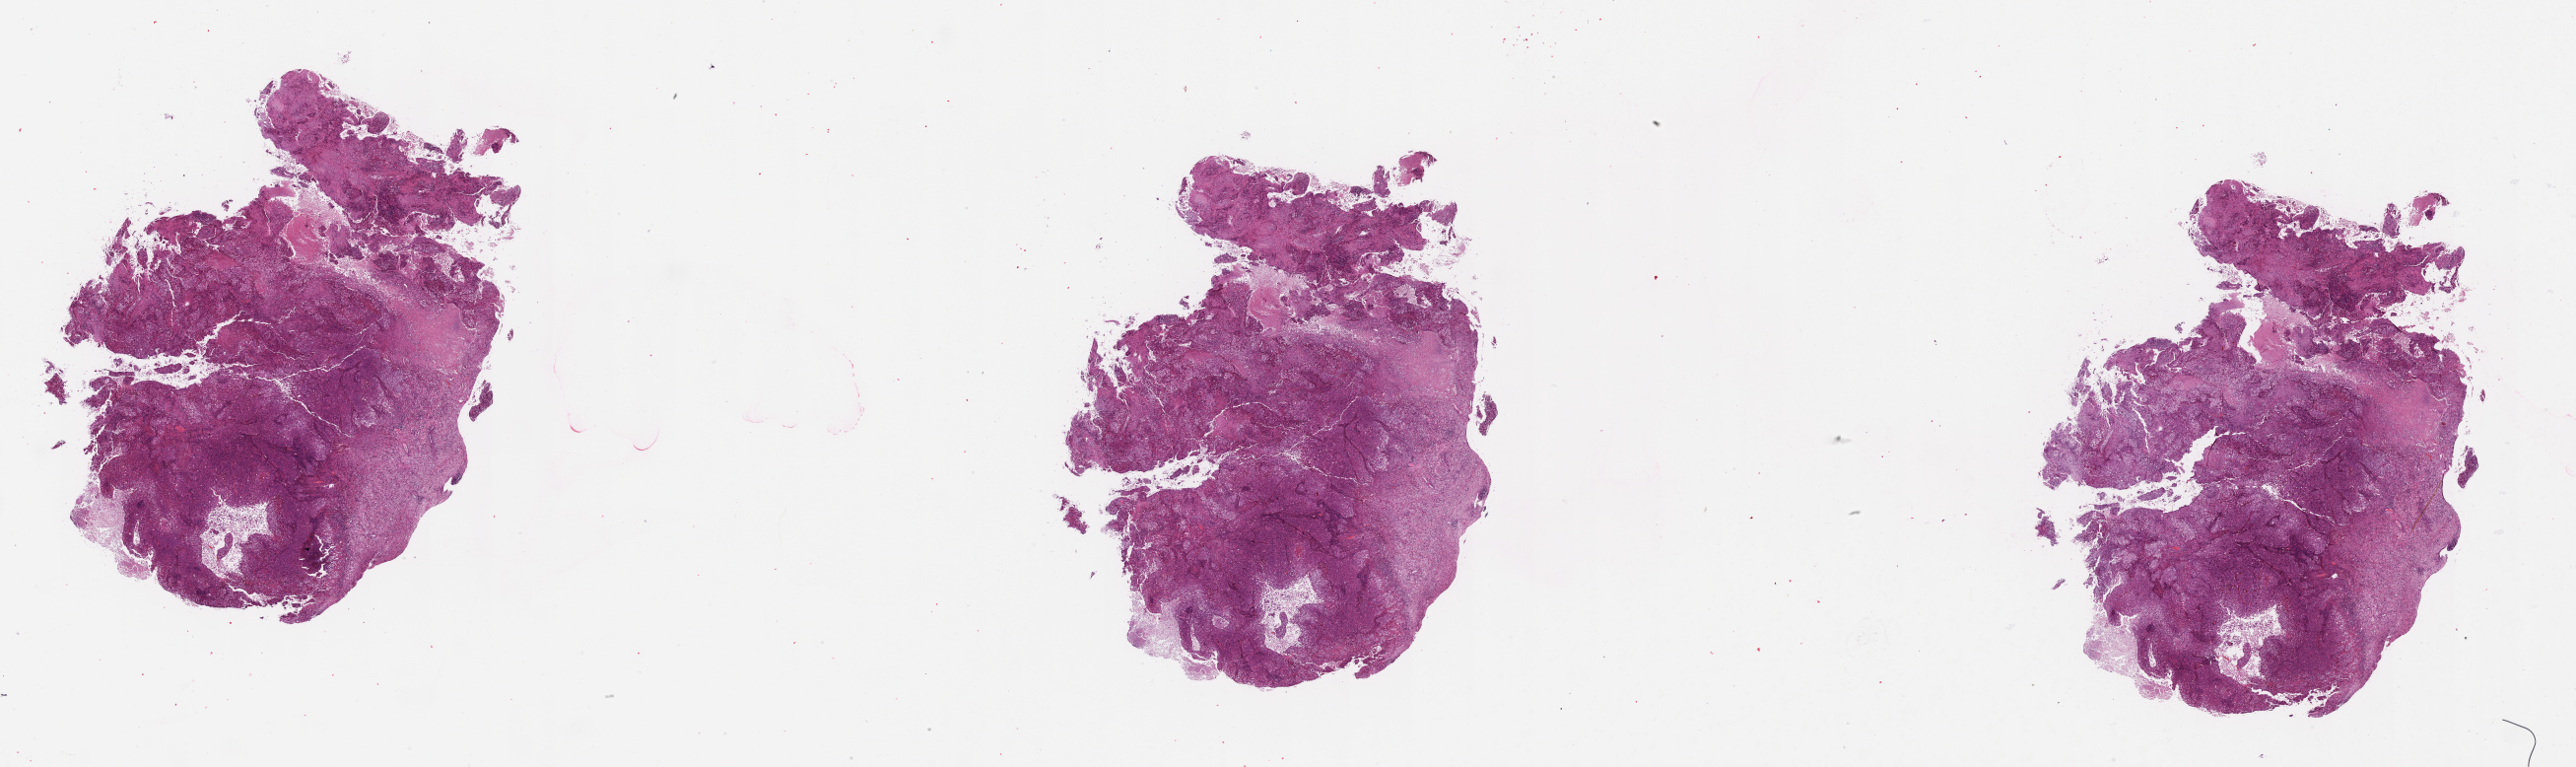
Whole-slide histology image, H&E-stained — shown as a low-resolution overview of the whole scanned area (about 42.1 x 12.5 mm, acquisition: 20x scan), lung, tissue type not recorded.
• patient diagnosis (cohort enrolment): lung adenocarcinoma (lung)